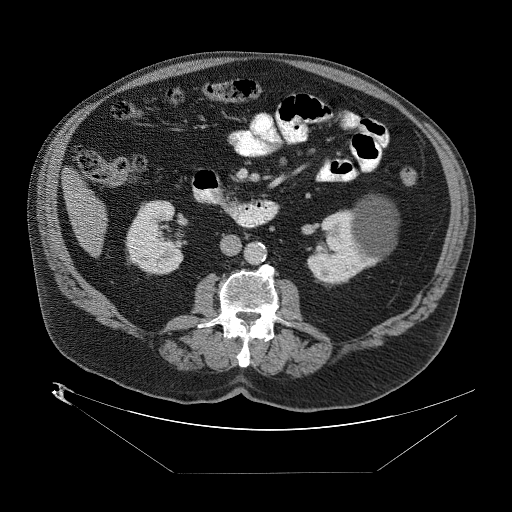
Contrast-enhanced abdominal CT (liver protocol), one axial slice. Position 10 of 89 along the scan axis. Reconstruction kernel STANDARD. 140 kVp. One of 2 acquisitions stored at this slice position. Soft-tissue window (W 400 / L 40 HU). 512 × 512 image matrix, field of view 480 × 480 mm. Case-level facts recorded for this patient, not image findings: diagnosis: hepatocellular carcinoma (patient treated with transarterial chemoembolisation; whether this scan precedes or follows treatment is not stated here); TNM stage (as recorded): Stage-II; Child-Pugh class: B; tumour differentiation: moderately differentiated.
Structures marked on this image (semi-automatically segmented with operator editing):
- abdominal aorta: box from (x=245, y=242) to (x=267, y=265) px
- liver parenchyma outside the tumour (the mass and vessels are separate outlines, so this box may not span the whole liver): (x=62, y=163)–(x=106, y=252)